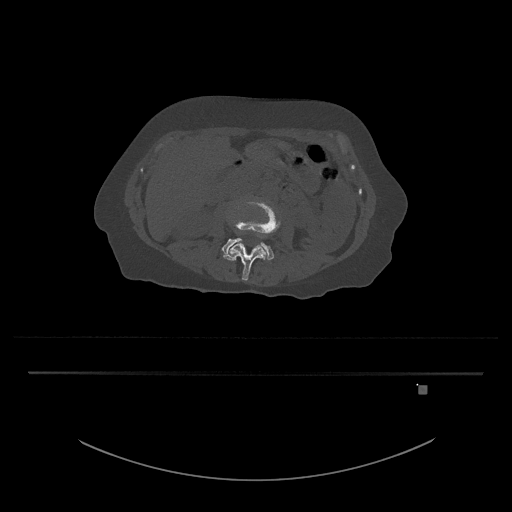
CT including the spine, one axial slice. Position 404 of 797 along the scan axis. Reconstruction kernel Br40s/3. Bone window (W 1800 / L 400 HU). 512 × 512 image matrix, field of view 500 × 500 mm. Patient: female, 57 years. Case-level facts recorded for this patient, not image findings: primary cancer: cervical.
Structures marked on this image (semi-automatically segmented with operator editing):
- L3 vertebra: bounding box (x1, y1, x2, y2) in pixels: (223, 201, 280, 281)
- L4 vertebra: (222, 238, 274, 261)